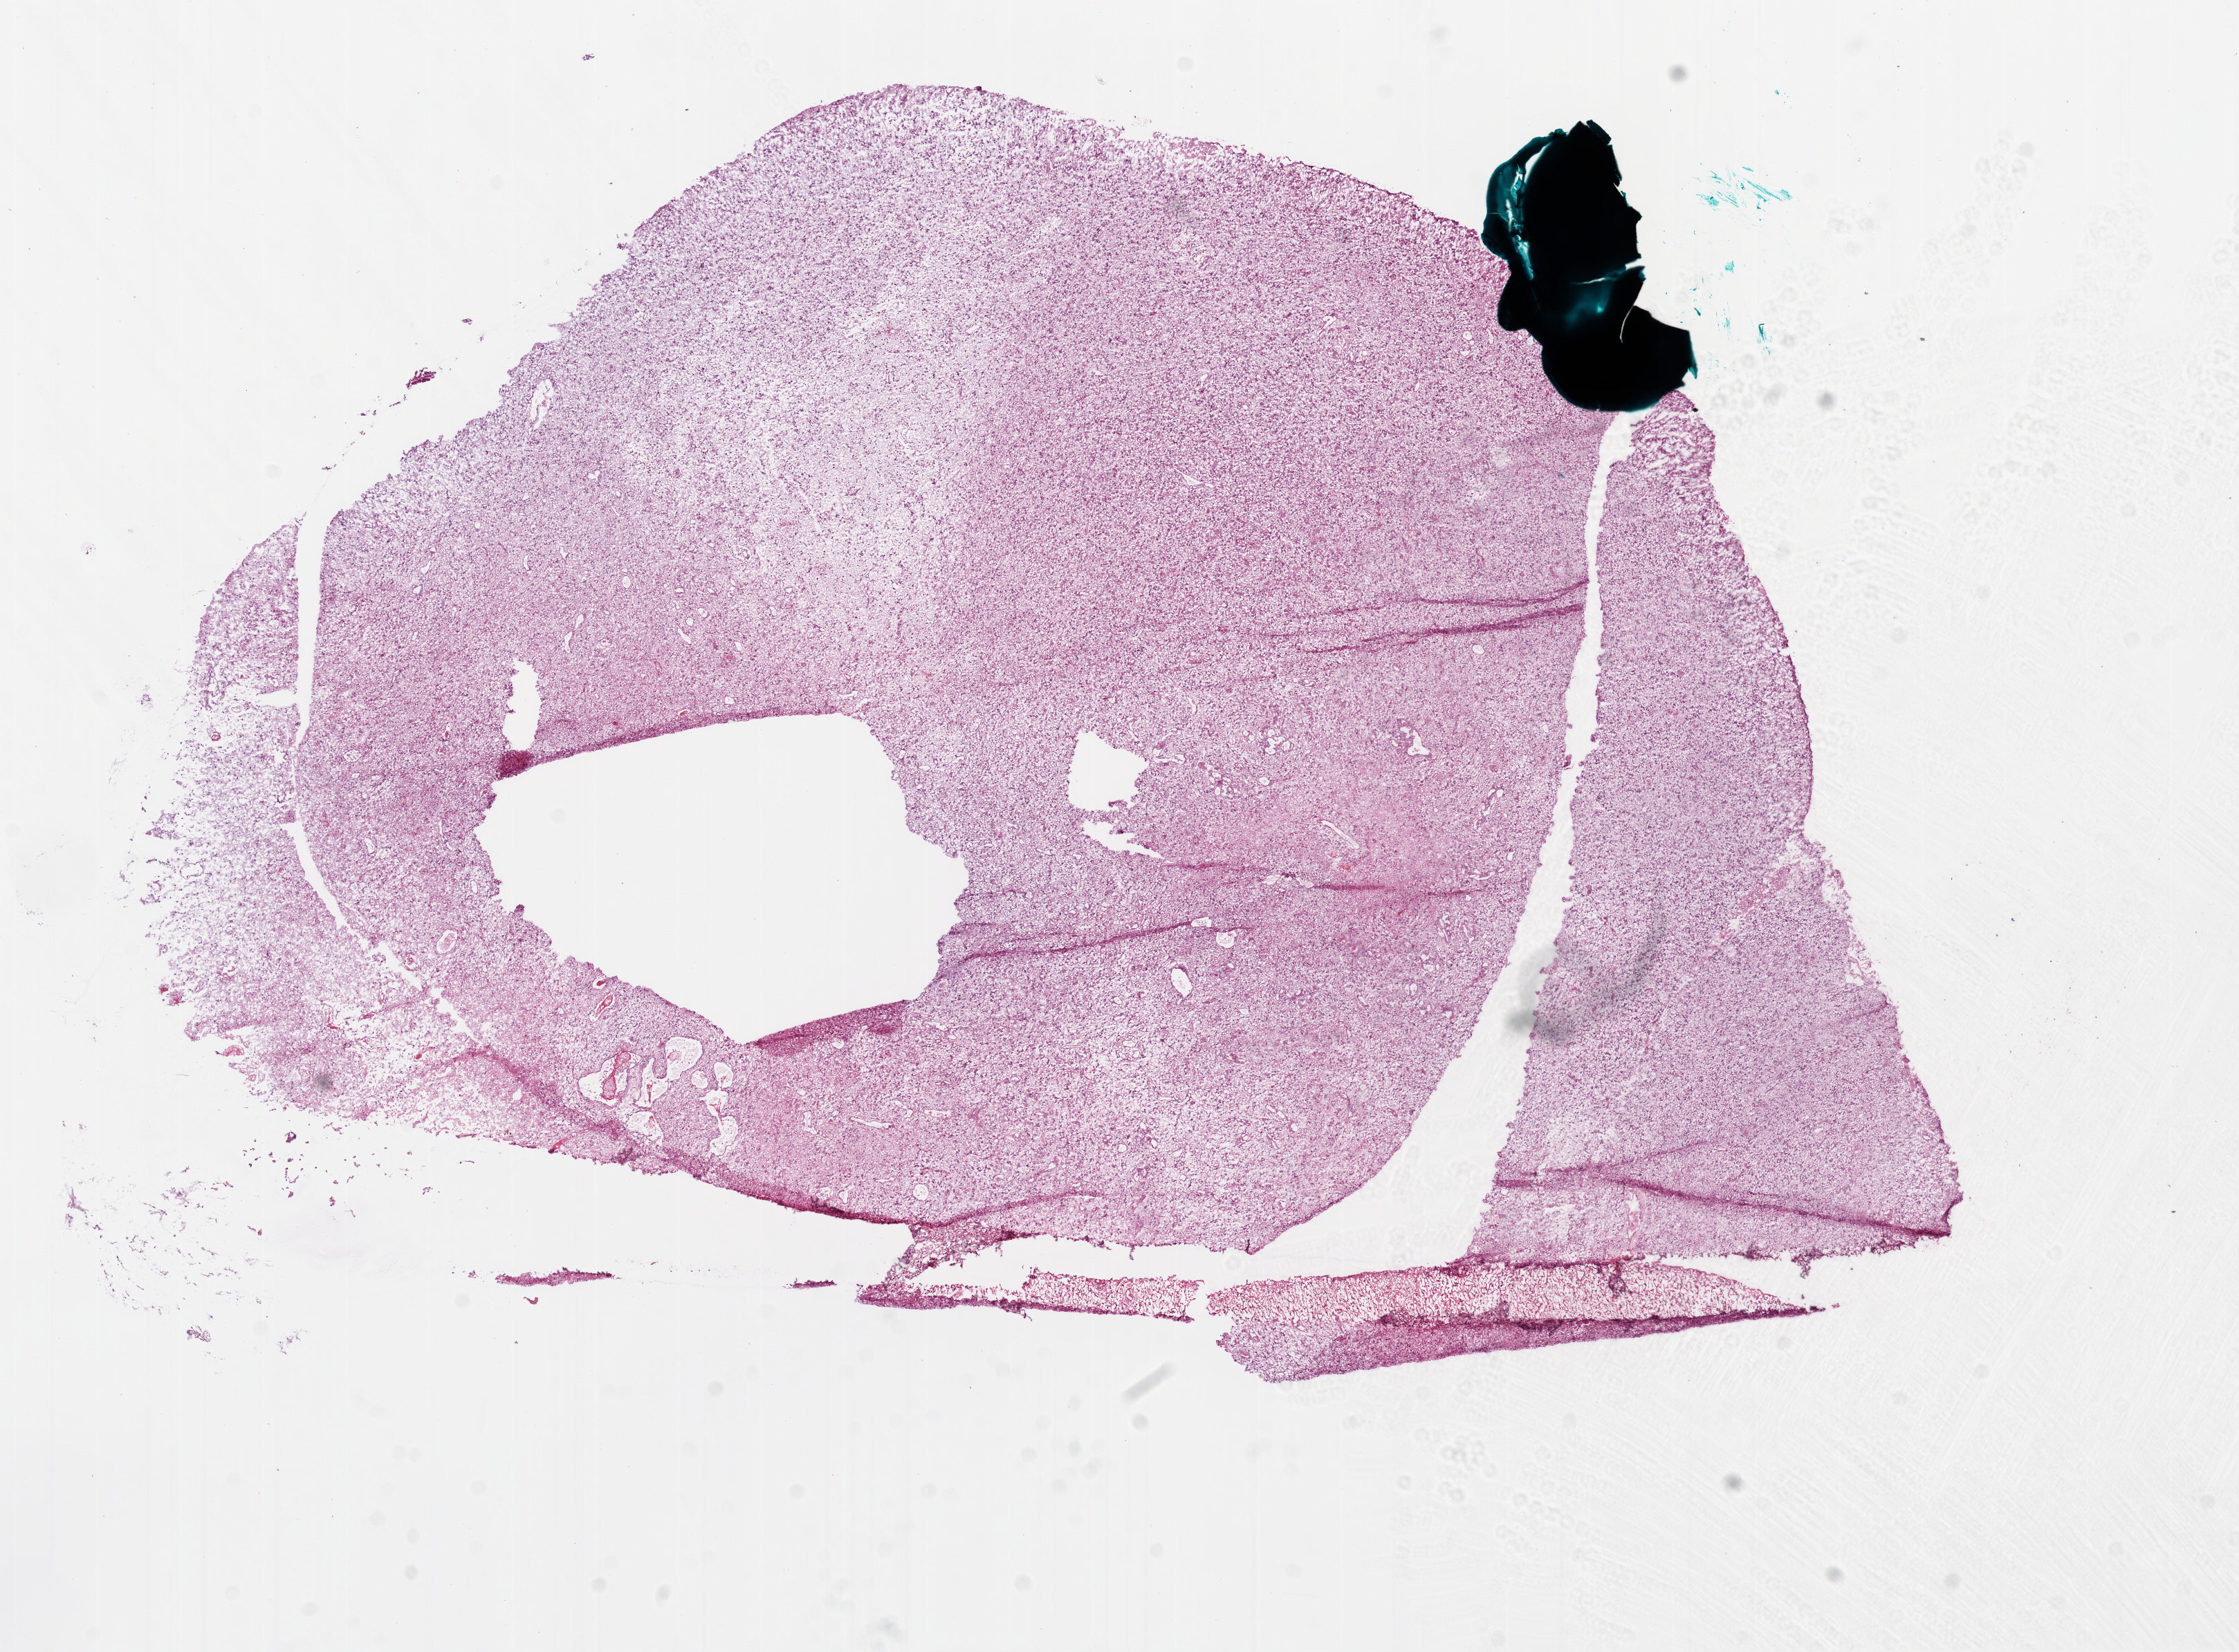
Digitized Hematoxylin and eosin (H&E) stained tissue section (whole slide), shown as a low-resolution overview of the whole scanned area (about 13.1 x 9.6 mm), frozen section from the bottom of the tissue portion, primary tumour sample from the brain. Male patient; age at initial diagnosis 55 years. Slide review estimates, as recorded: tumour cells 80%, tumour nuclei 90%, normal cells 0%, stromal cells 0%, necrosis 20%. Infiltration values recorded for this section: neutrophil infiltration 100%.
Diagnosis: Glioblastoma.